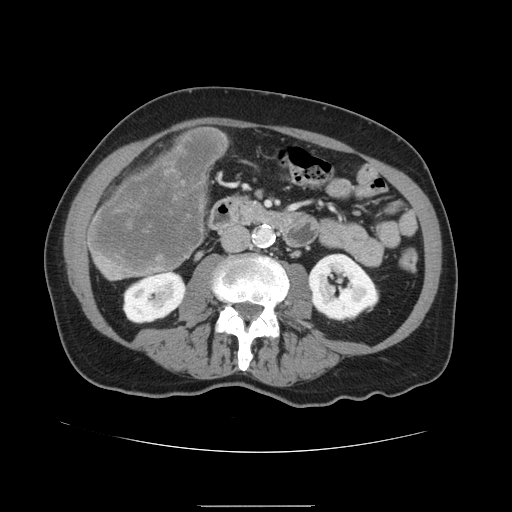
Contrast-enhanced abdominal CT, one axial slice. Position 37 of 168 along the scan axis. 120 kVp. Intravenous contrast given. Soft-tissue window (W 400 / L 40 HU). 2.5 mm slice thickness. 512 × 512 image matrix. Male patient, age 74 years. Case-level facts recorded for this patient, not image findings: diagnosis: colorectal cancer liver metastases, imaged before liver resection; multiple liver metastases: no; largest metastasis: 14.5 cm.
Outlined on this slice (outlined manually by an expert reader):
- liver: box from (x=88, y=127) to (x=228, y=280) px
- liver metastasis: (x=90, y=132)–(x=225, y=274)